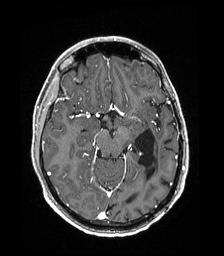
Brain MRI from a brain-tumour surgery series, one axial slice; T1-weighted post-contrast; 1 mm slice thickness; 224 × 256 image matrix. From the clinical record (not read from this slice): histopathology: Low grade glioma; IDH mutation: no; tumour location: Left Parieto-Occipital Intraventricular.
Structures marked on this image (expert manual segmentation):
- previous resection cavity: bounding box (x1, y1, x2, y2) in pixels: (134, 130, 156, 179)